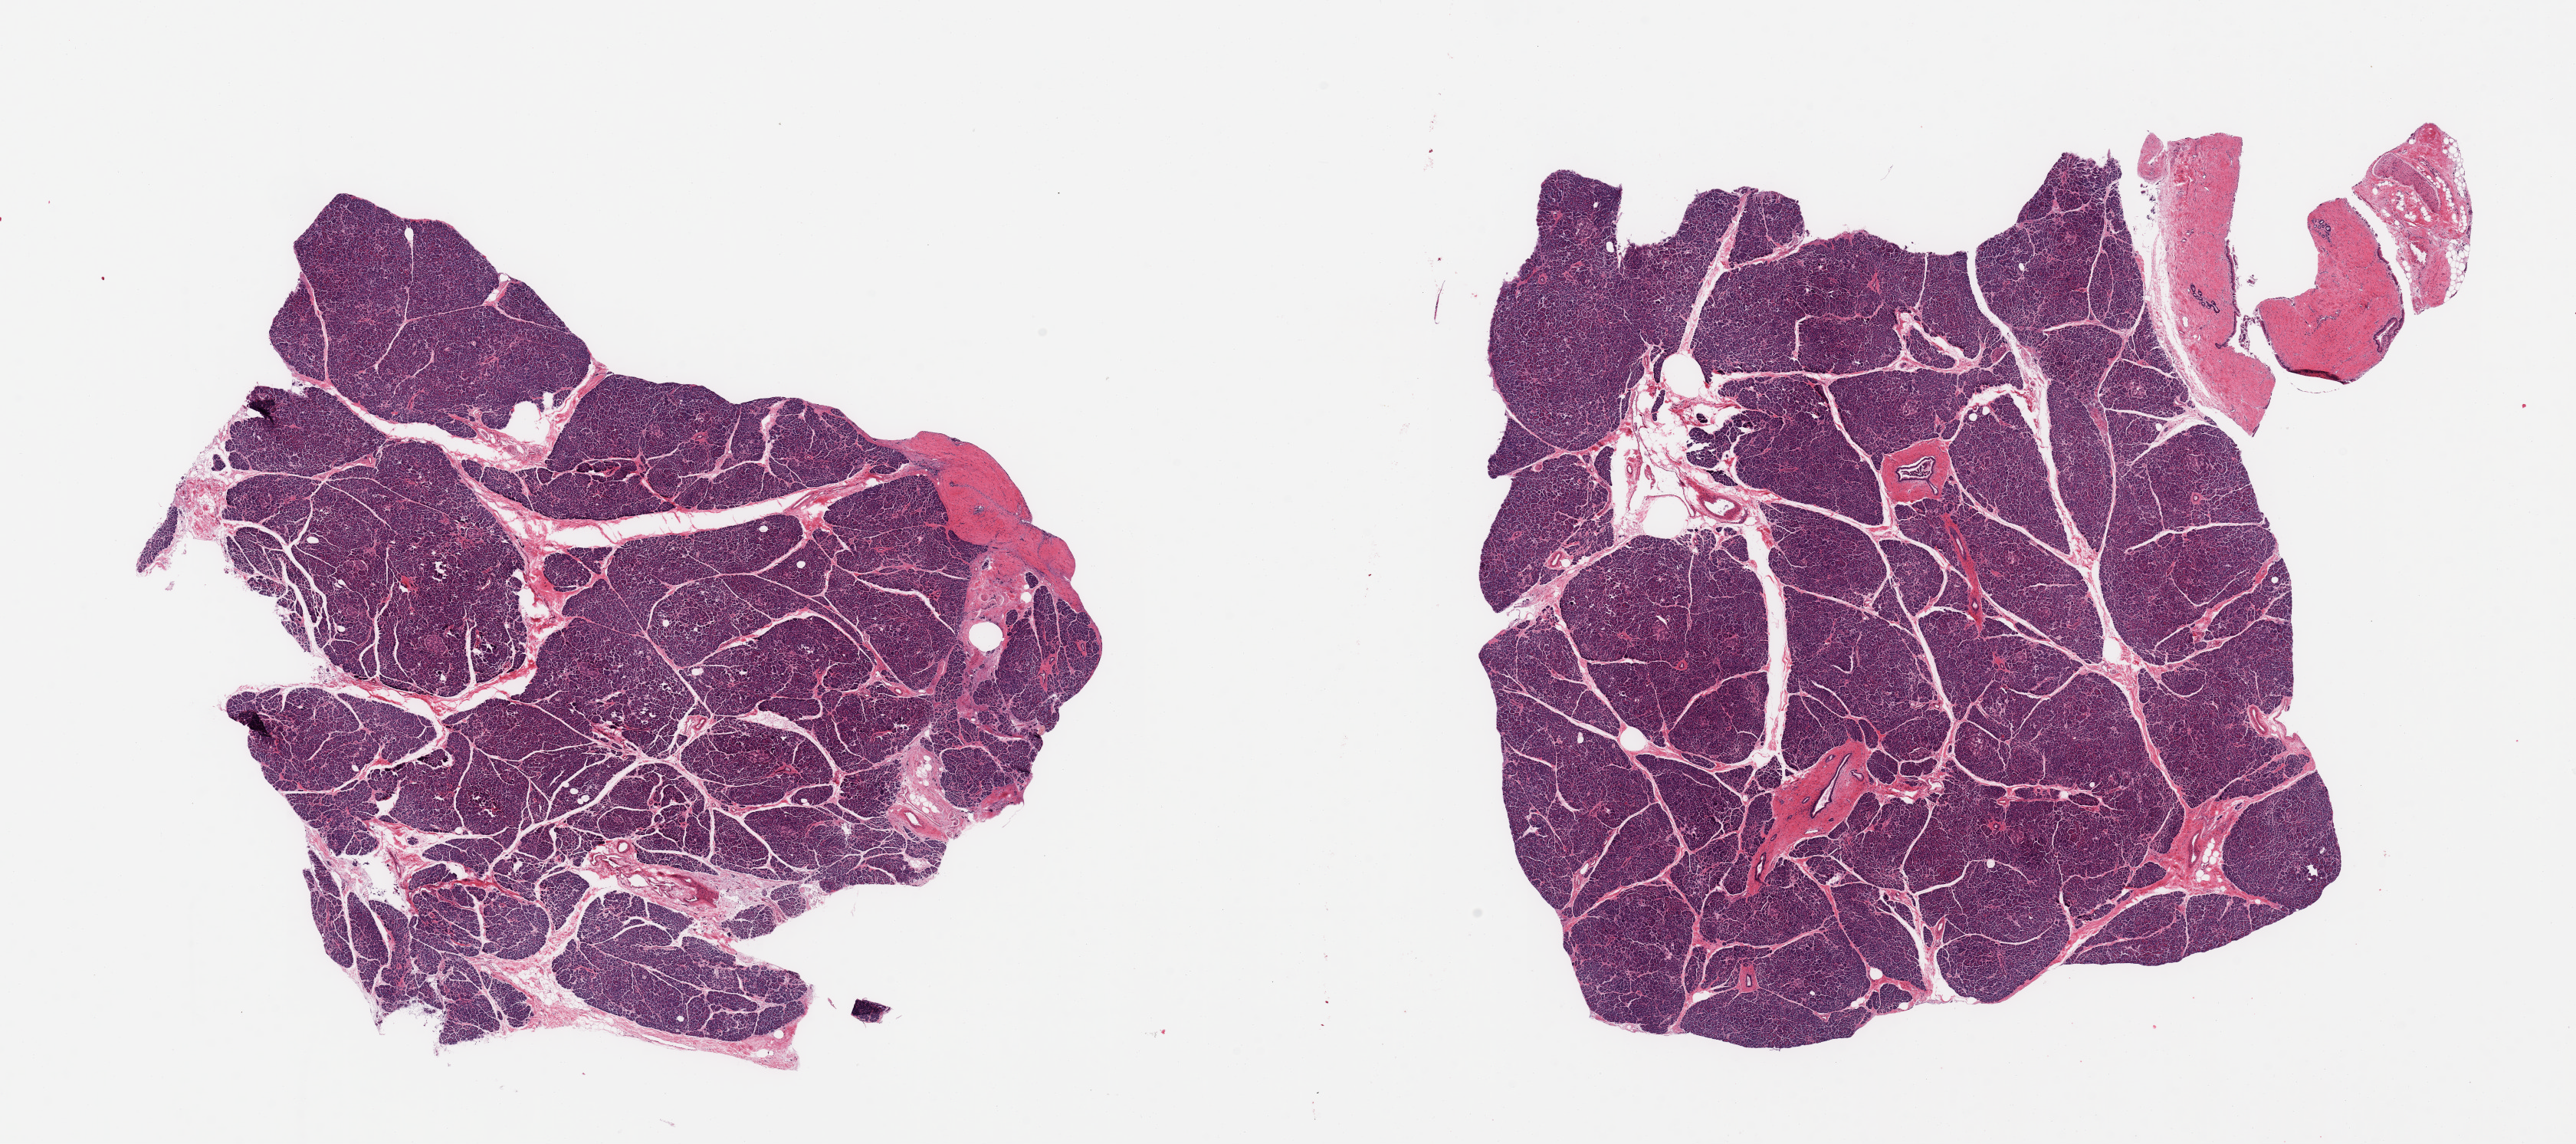
Whole-slide image, haematoxylin and eosin stain — whole scanned area (about 26.6 x 11.8 mm) shown as a low-resolution overview, PAXgene-fixed, paraffin-embedded tissue, sampled site (target tissue): pancreas, tissue donor sample. Donor sex: female.
Pathologist's review note for this sample: 2 pieces; essentially well preserved parenchyma; Langerhans islets present; attached dense fibrous tissue with ductal structures and fibroadipose tissue with nerves.